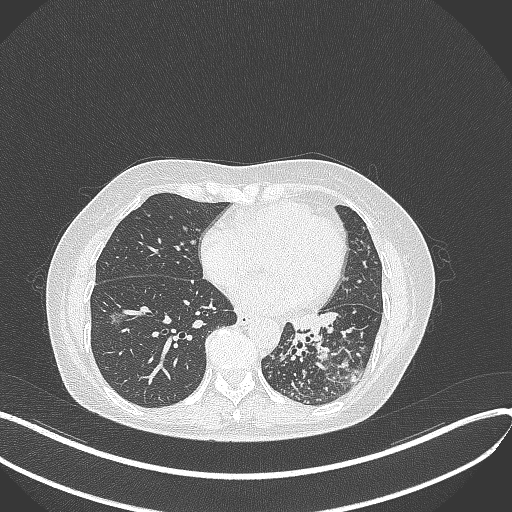
Chest CT, one axial slice. Position 157 of 429 along the scan axis. Reconstruction kernel B70f. Lung window (W 1500 / L -600 HU). 1 mm slice thickness. 512 × 512 image matrix. Female patient, age 63 years. Case-level facts recorded for this patient, not image findings: clinical TNM (as recorded): T1b N0 M0.
Outlined on this slice (bounding box drawn by a radiologist):
- lung tumour (recorded histology: adenocarcinoma): box from (x=281, y=305) to (x=343, y=348) px